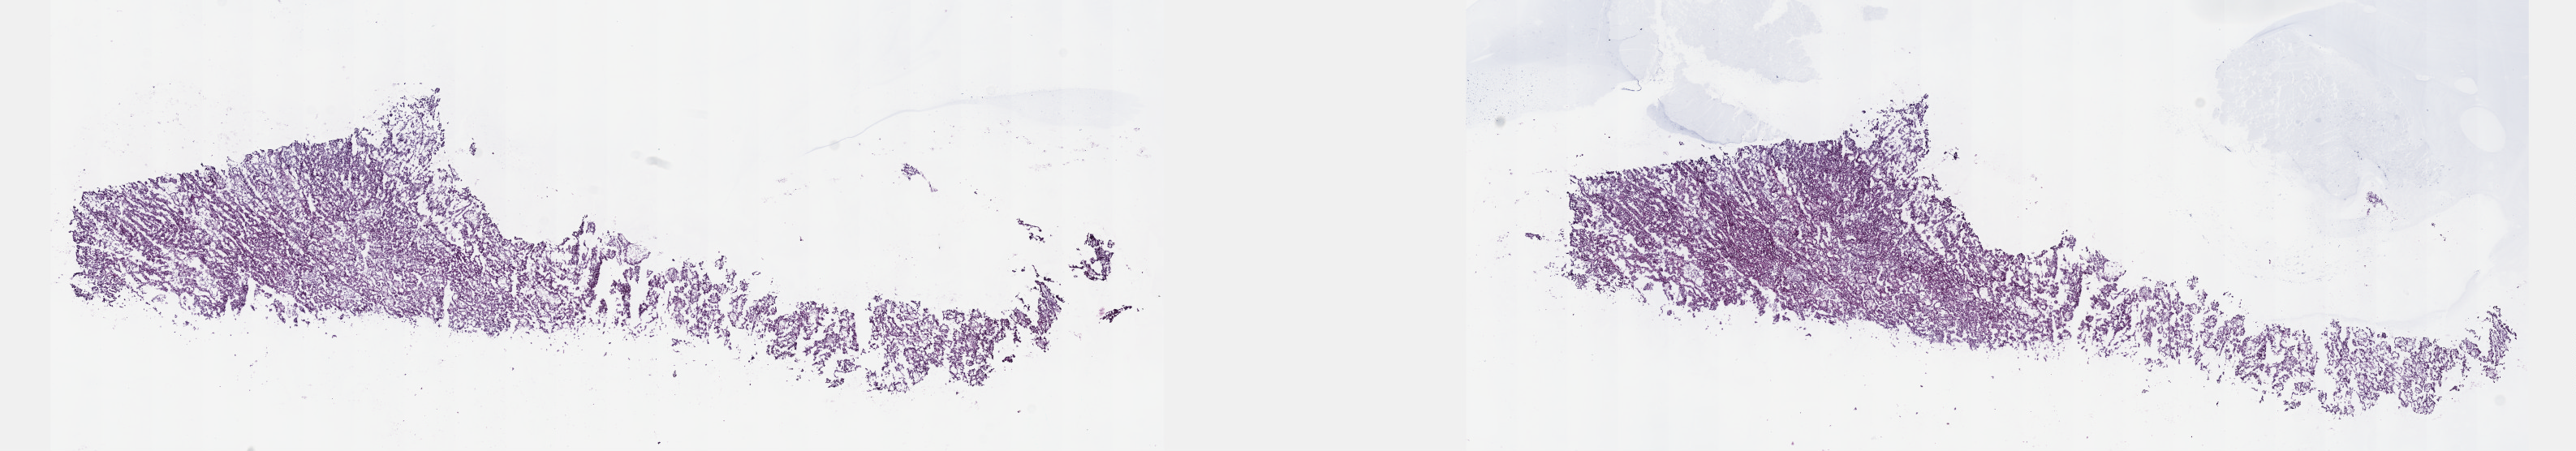
Whole-slide histology image, Hematoxylin and eosin (H&E) stained — low-resolution overview of the scanned area, about 25.7 x 4.5 mm; frozen section from the top of the tissue portion; sample: primary tumour, kidney. Male patient; age at initial diagnosis 63 years. Slide review estimates, as recorded: tumour cells 100%, tumour nuclei 80%, normal cells 0%, stromal cells 0%, necrosis 0%. Inflammatory infiltration, as recorded: lymphocyte infiltration 1%, monocyte infiltration 2%, neutrophil infiltration 0%.
Diagnosis: Papillary adenocarcinoma, NOS. AJCC pathologic stage: I (7th edition).